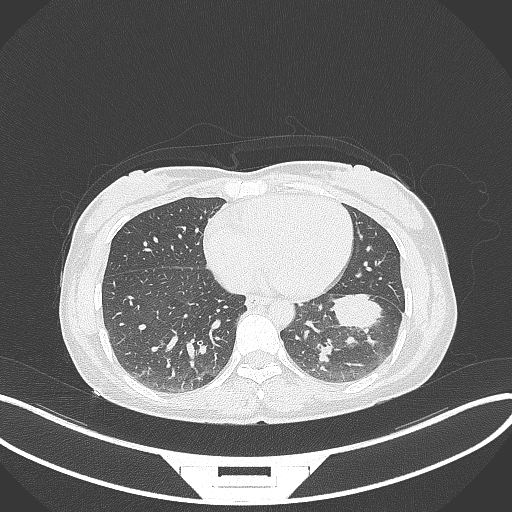
Chest CT, one axial slice; lung window (W 1500 / L -600 HU); 1 mm slice thickness; 512 × 512 image matrix, field of view 400 × 400 mm. Female patient, age 41 years. Case-level facts recorded for this patient, not image findings: clinical TNM (as recorded): T2a N3 M1b.
Structures marked on this image (bounding box drawn by a radiologist):
- lung tumour (recorded histology: adenocarcinoma): bounding box (x1, y1, x2, y2) in pixels: (325, 290, 388, 337)